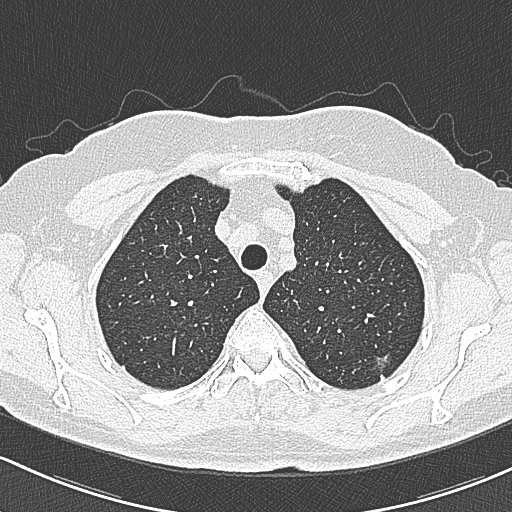
Axial slice from a low-dose chest CT screening exam. First (baseline) screen. Lung window (W 1500 / L -600 HU). Lung (sharp) reconstruction kernel (B80f). Slice 55 of 312 in the series. Female, age 65 years at enrolment. Current smoker at enrolment.
Lesion marked by an expert reader, bounding box (x1, y1, x2, y2) in pixels: (367, 343, 404, 383). The screening reader recorded 3 non-calcified nodules or masses ≥4 mm on this exam (left upper lobe, left upper lobe, right upper lobe); which of them this box marks is not recorded. Lung cancer was diagnosed 390 days after this screen: bronchiolo-alveolar carcinoma, non-mucinous, left upper lobe, stage IA (AJCC 6th edition), 10 mm at pathology.